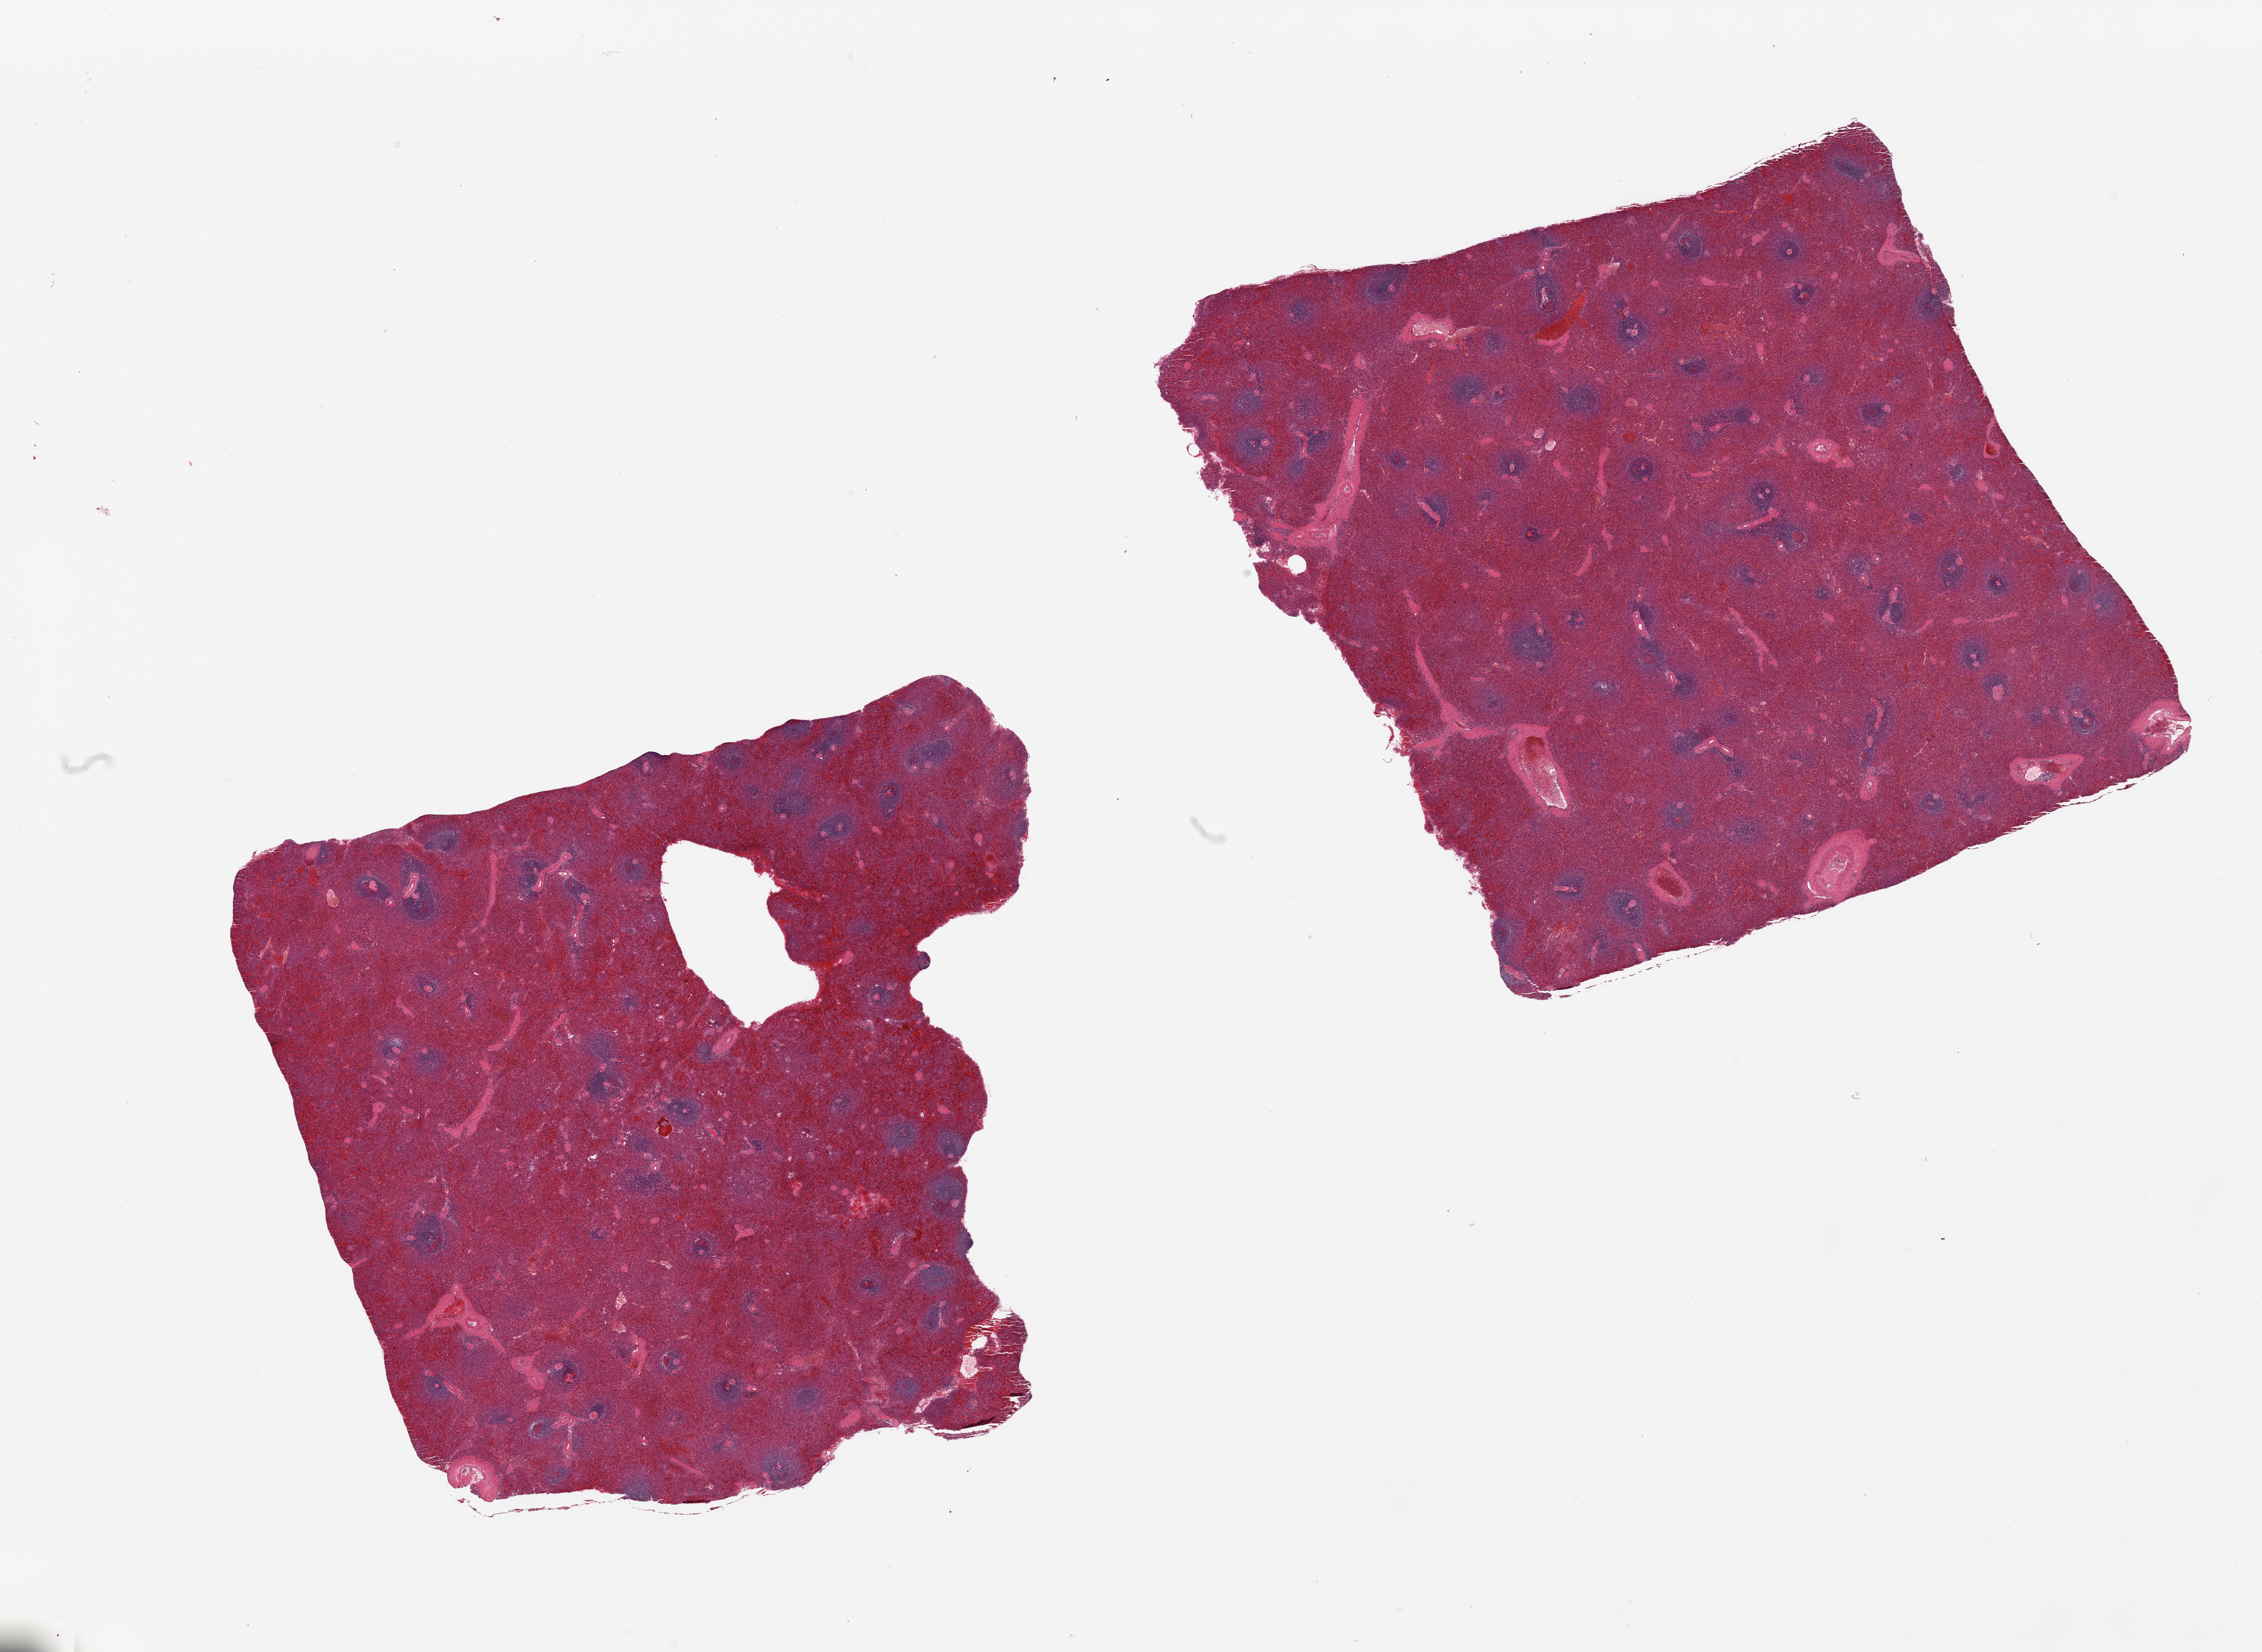
Hematoxylin and eosin (H&E) whole-slide image, low-resolution overview of the scanned area, about 30.5 x 22.3 mm. PAXgene-fixed paraffin-embedded (PFPE) section. Section of spleen (target tissue). Tissue donor sample. Female donor.
• pathologist's review note for this sample: 2 pieces, mild congestion